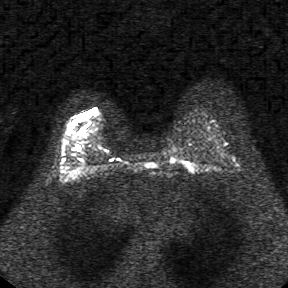
Breast MRI, one axial slice. Slice 24 of 34 in the series (ordered by position). Diffusion-weighted series; image 2 of 4 stored at this slice position (different b-values; order by instance number). 1.5 T. 288 × 288 image matrix. Female patient.
Structures marked on this image (outlined manually by an expert reader):
- tumour on diffusion-weighted imaging: bounding box (x1, y1, x2, y2) in pixels: (77, 107, 96, 119)